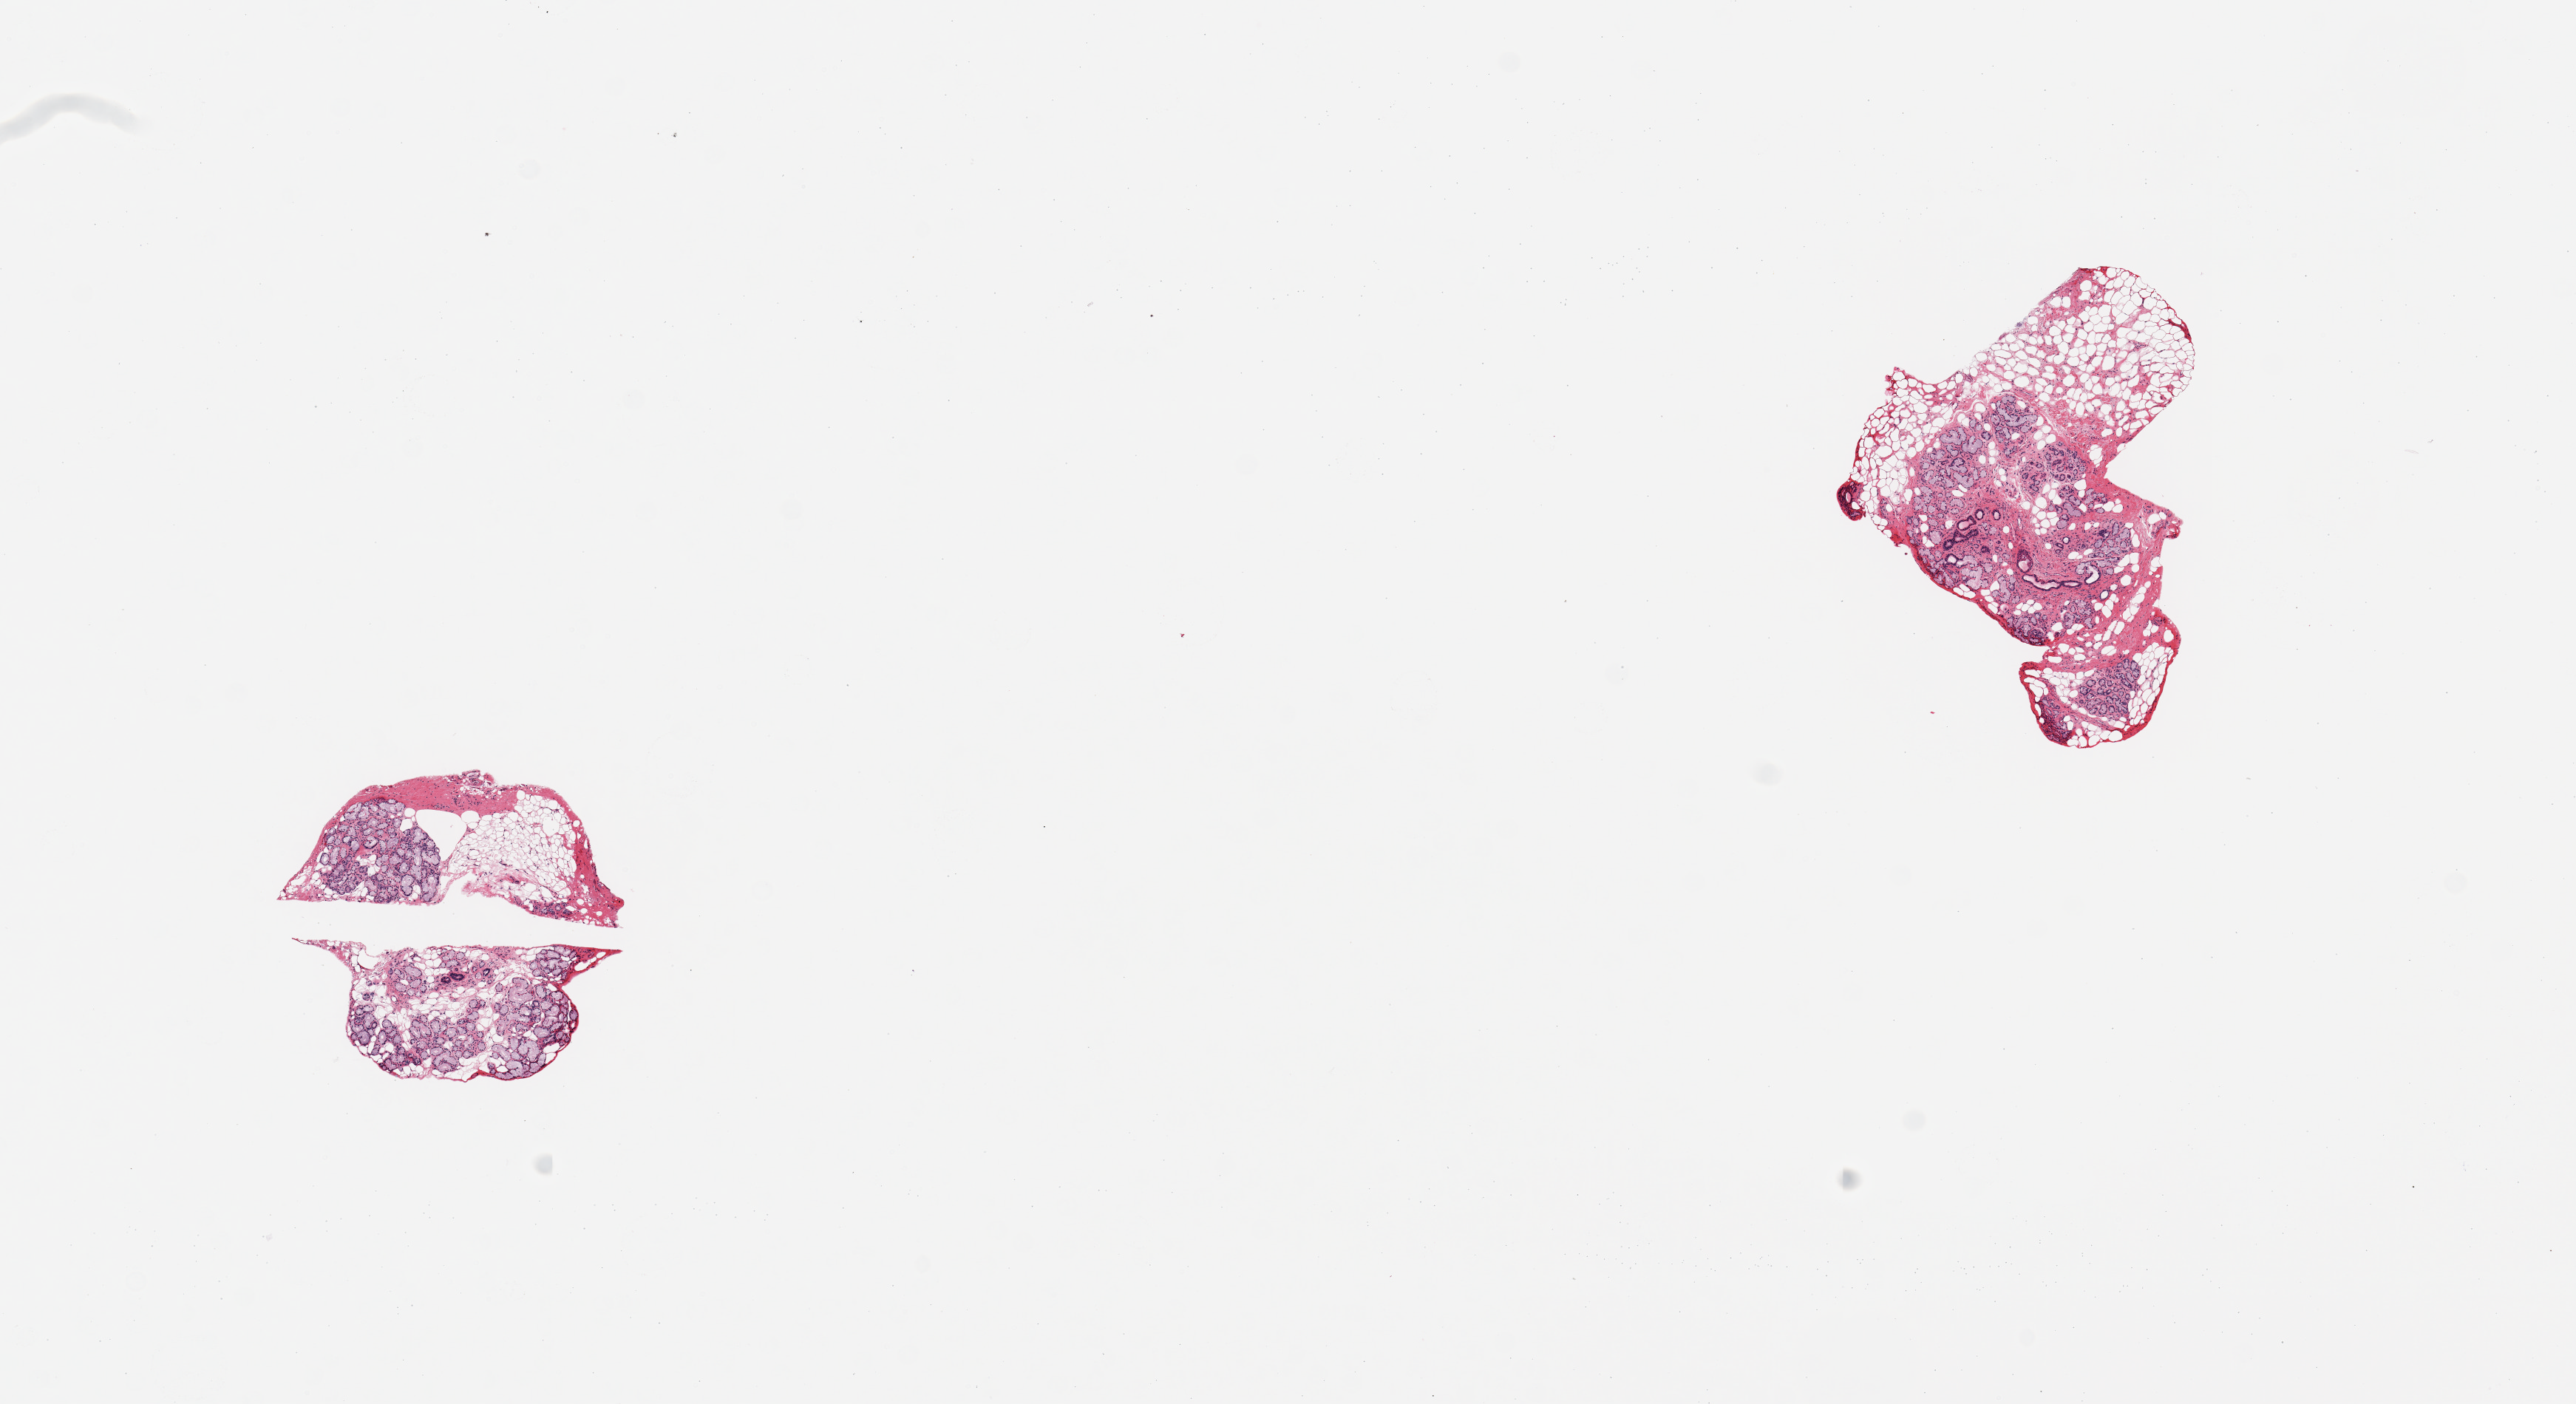
Digitized hematoxylin and eosin (H&E)-stained section, shown as a low-resolution overview of the whole scanned area (about 13.8 x 7.5 mm). PAXgene-fixed, paraffin-embedded tissue. Section of minor salivary gland (target tissue). Tissue donor sample. Male donor.
Reviewer comment on this tissue sample: 2 pieces;~60% glandular and ductal elements and ~40% surrounding fat.